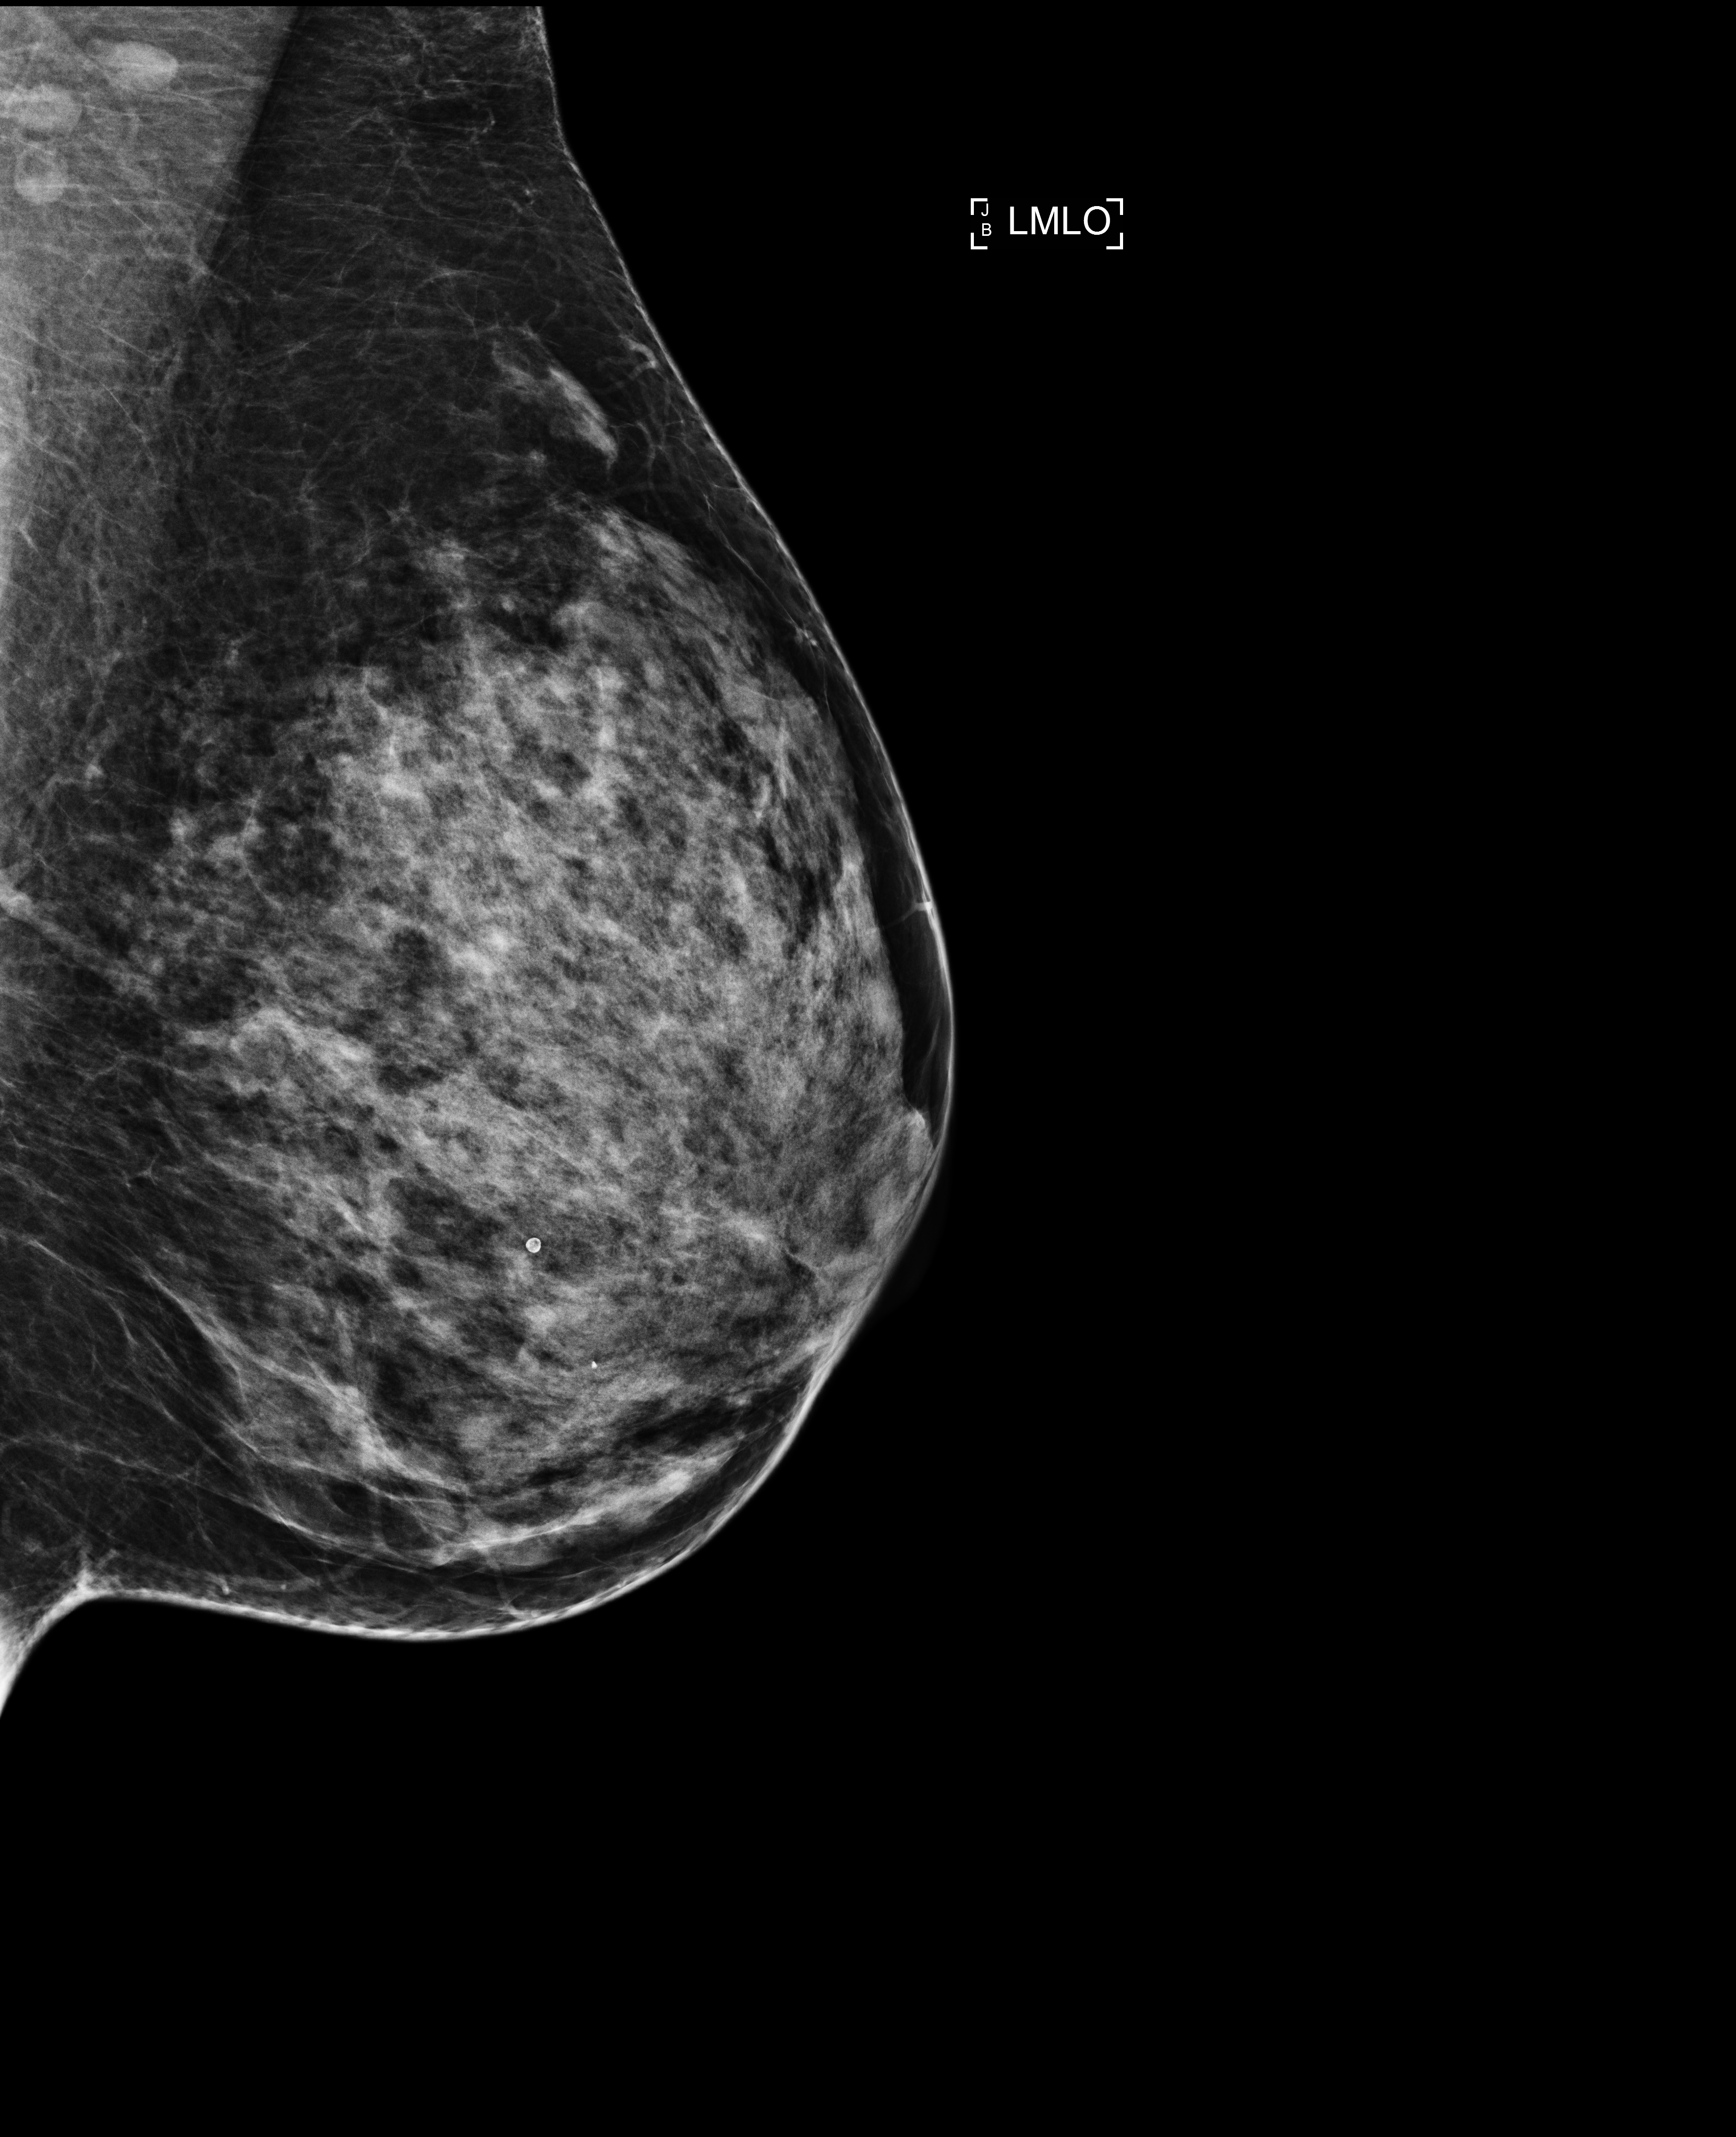
Annual screening mammography examination, system: Selenia Dimensions. Patient aged 42 years (female).
Image type: full-field digital mammogram. Breast: left. Projection: medio-lateral oblique projection.